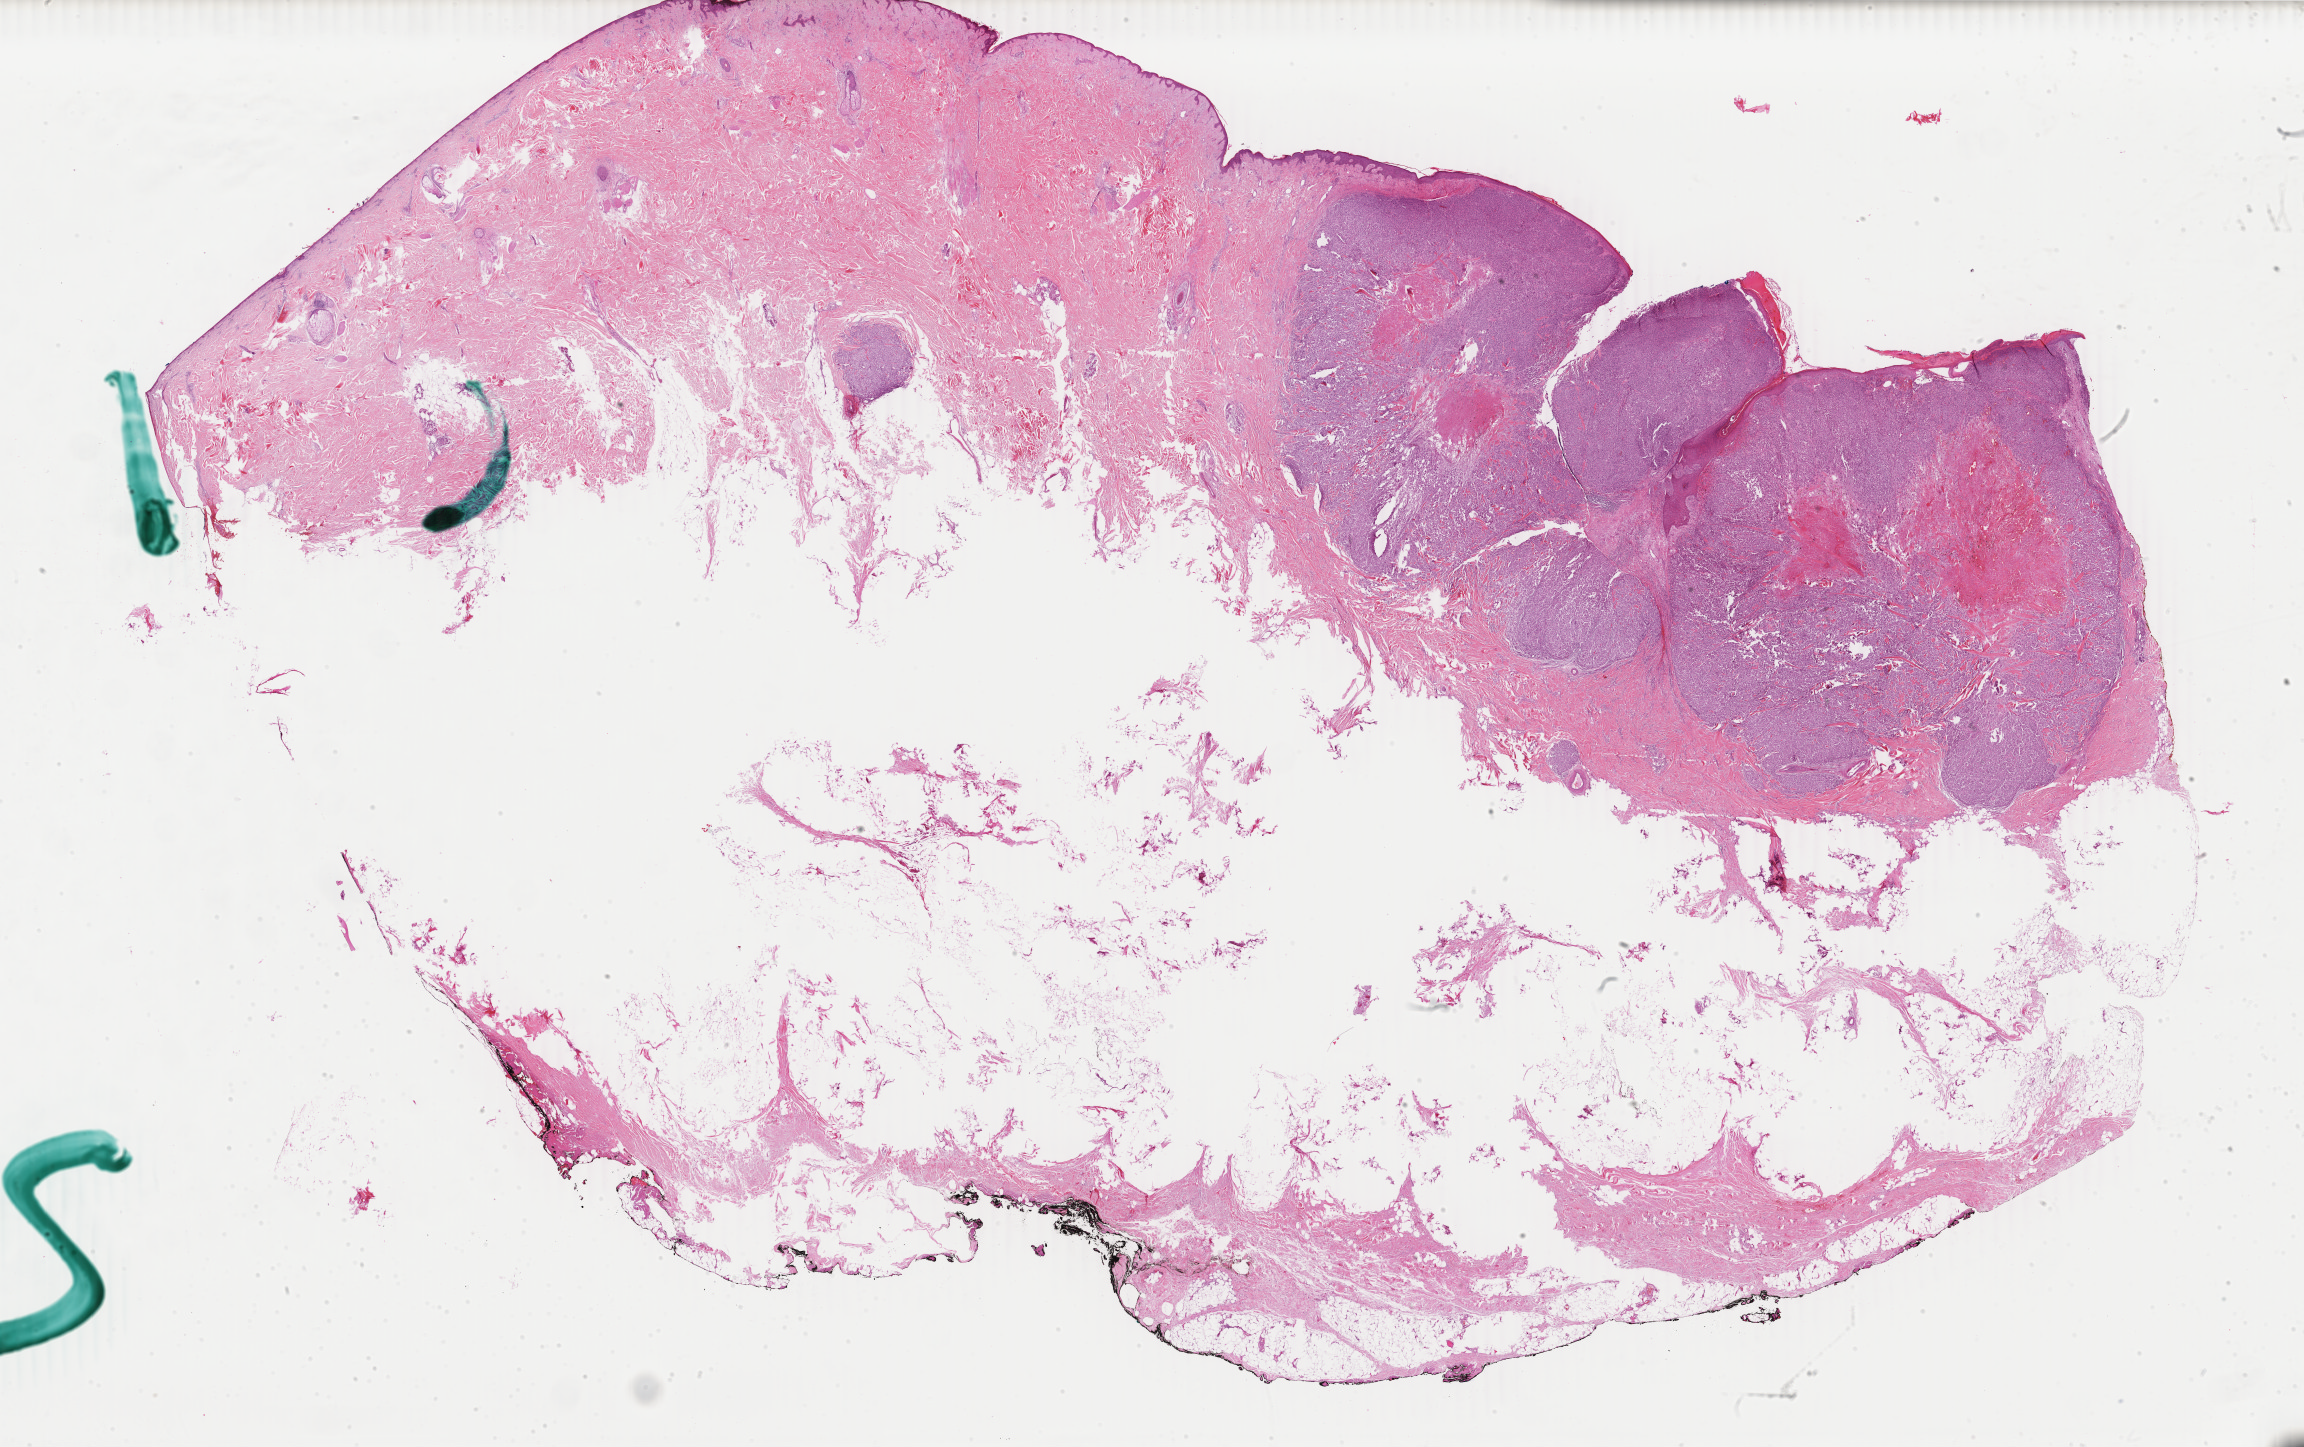
Whole-slide histology image, Hematoxylin and eosin (H&E) stained — low-resolution overview of the scanned area, about 36.6 x 23.0 mm (slide scanned at 40x). Formalin-fixed paraffin-embedded (FFPE) diagnostic section. Sample: primary tumour, skin. Male, age 71 years at initial diagnosis.
Pathologic diagnosis: Malignant melanoma, NOS.